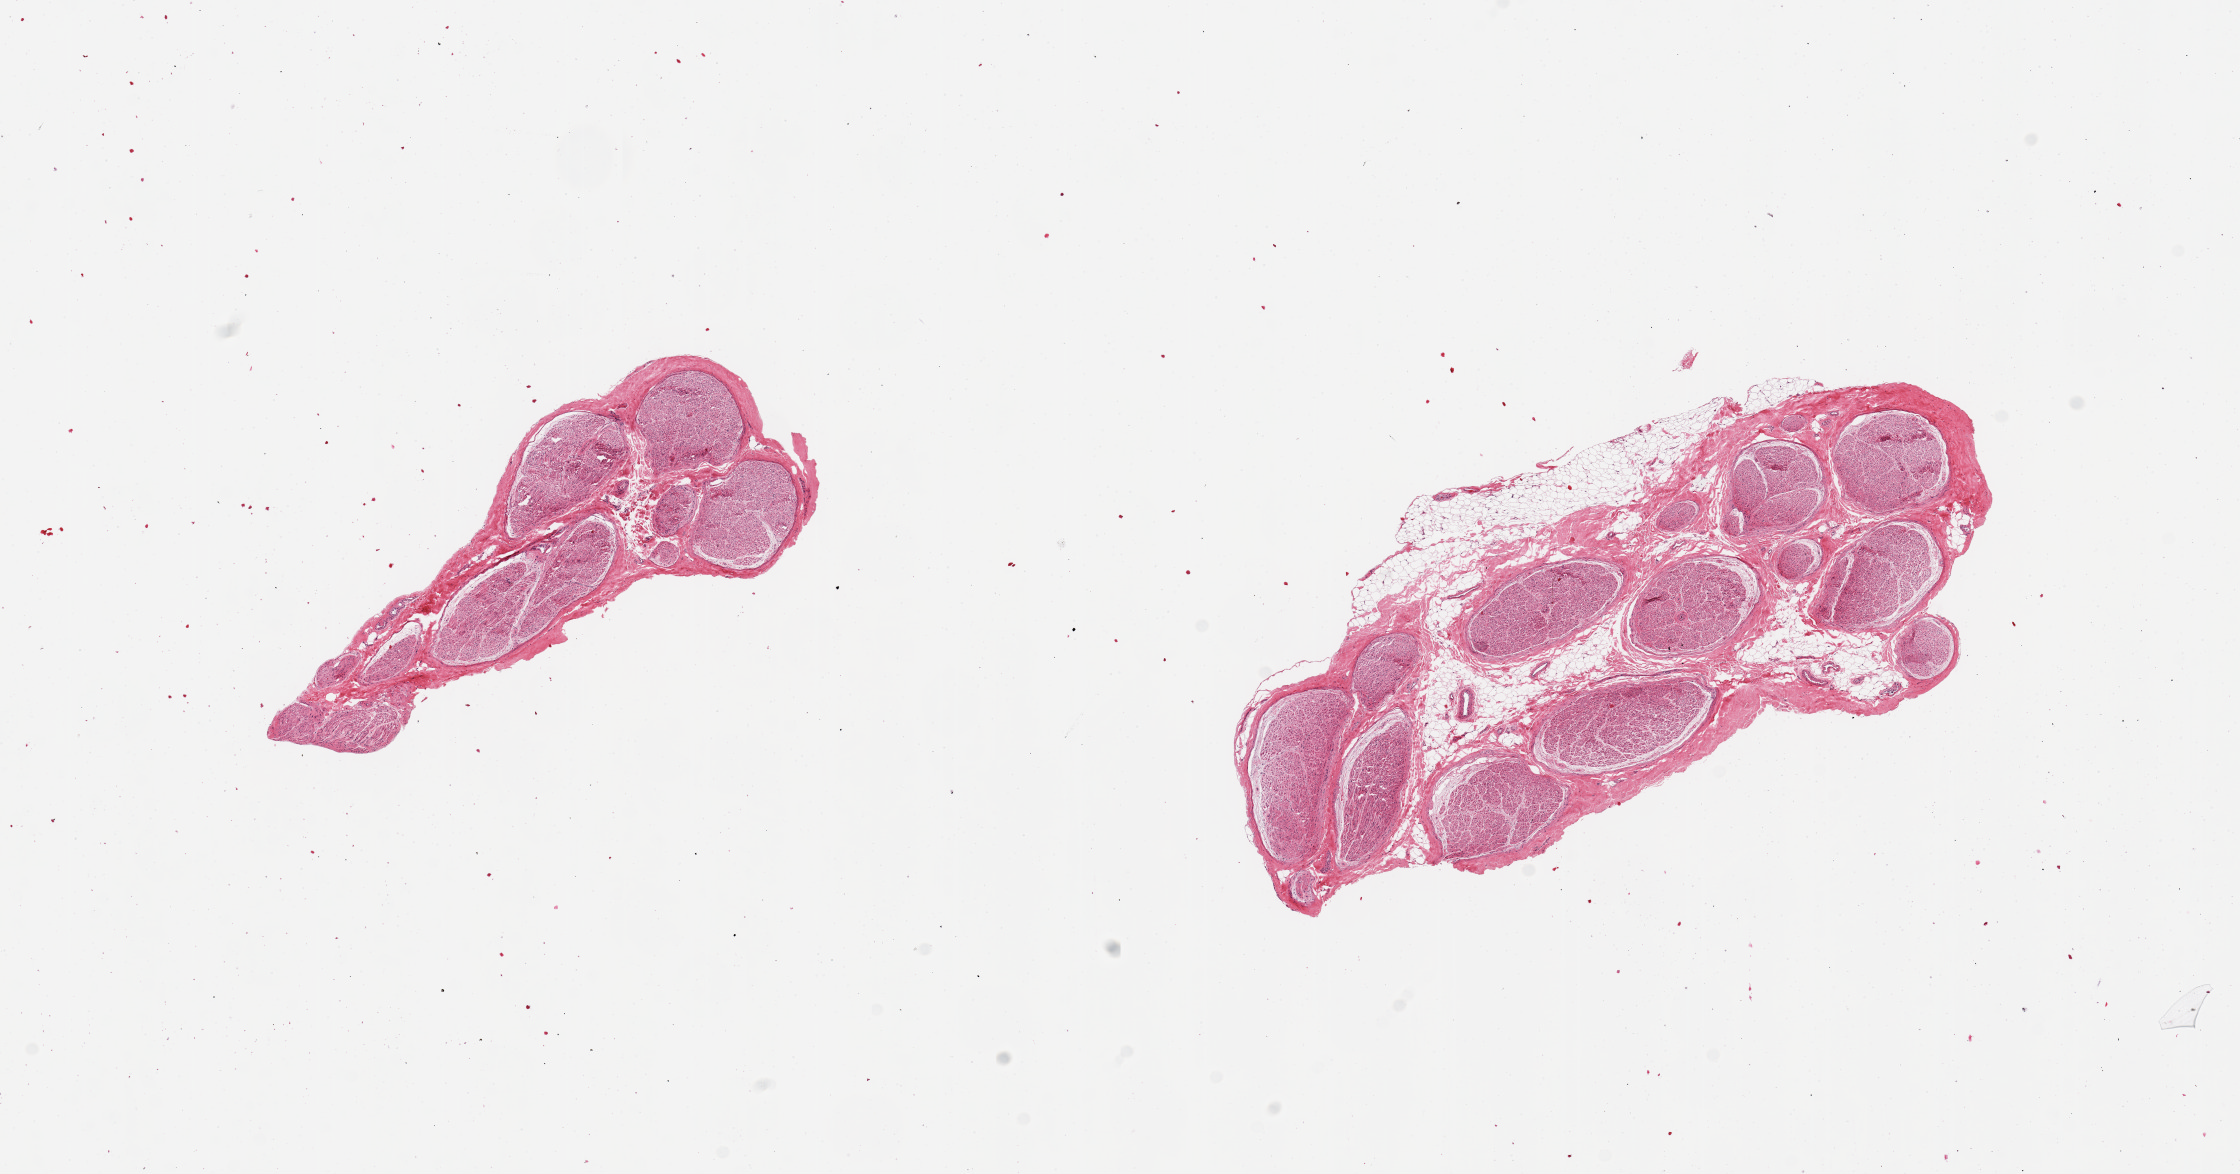
Haematoxylin and eosin whole-slide image, whole scanned area (about 17.7 x 9.3 mm, slide scanned at 20x) shown as a low-resolution overview, PAXgene-fixed paraffin-embedded (PFPE) section, section of tibial nerve (target tissue), tissue donor sample. Donor: male.
Reviewer comment on this tissue sample: 2 pieces; larger piece has 30% internal and external fat.